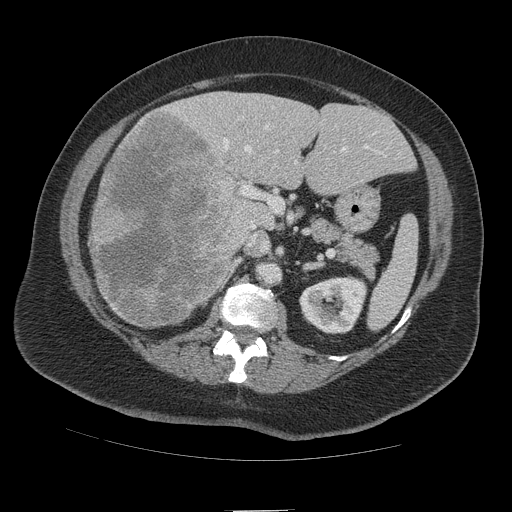
Contrast-enhanced abdominal CT (liver protocol), one axial slice. Position 55 of 109 along the scan axis. Soft-tissue window (W 400 / L 40 HU). 2.5 mm slice thickness. 512 × 512 image matrix. Case-level facts recorded for this patient, not image findings: diagnosis: hepatocellular carcinoma (patient treated with transarterial chemoembolisation; whether this scan precedes or follows treatment is not stated here); TNM stage (as recorded): Stage-IVB; Child-Pugh class: A; tumour differentiation: poorly differentiated; tumour nodularity: multinodular.
Structures marked on this image (semi-automatically segmented with operator editing):
- liver parenchyma outside the tumour (the mass and vessels are separate outlines, so this box may not span the whole liver): bounding box <90,92,412,328> (left, top, right, bottom; pixels)
- mass: <90,110,250,326>
- liver vessels: <223,125,382,249>